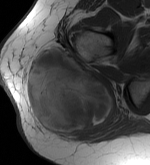
MRI of an extremity soft-tissue mass, one axial slice. MR volume resampled by the dataset authors to the PET/CT grid (not the native acquisition matrix). 150 × 165 image matrix, field of view 146 × 161 mm. Female patient. From the clinical record (not read from this slice): histological type: epithelioid sarcoma with vascular differentiation; site of the primary tumour: right buttock.
Structures marked on this image (expert contour drawn on MRI and transferred to this co-registered scan by the dataset authors):
- gross tumour volume (mass): bounding box [x1, y1, x2, y2] px = [25, 47, 115, 139]